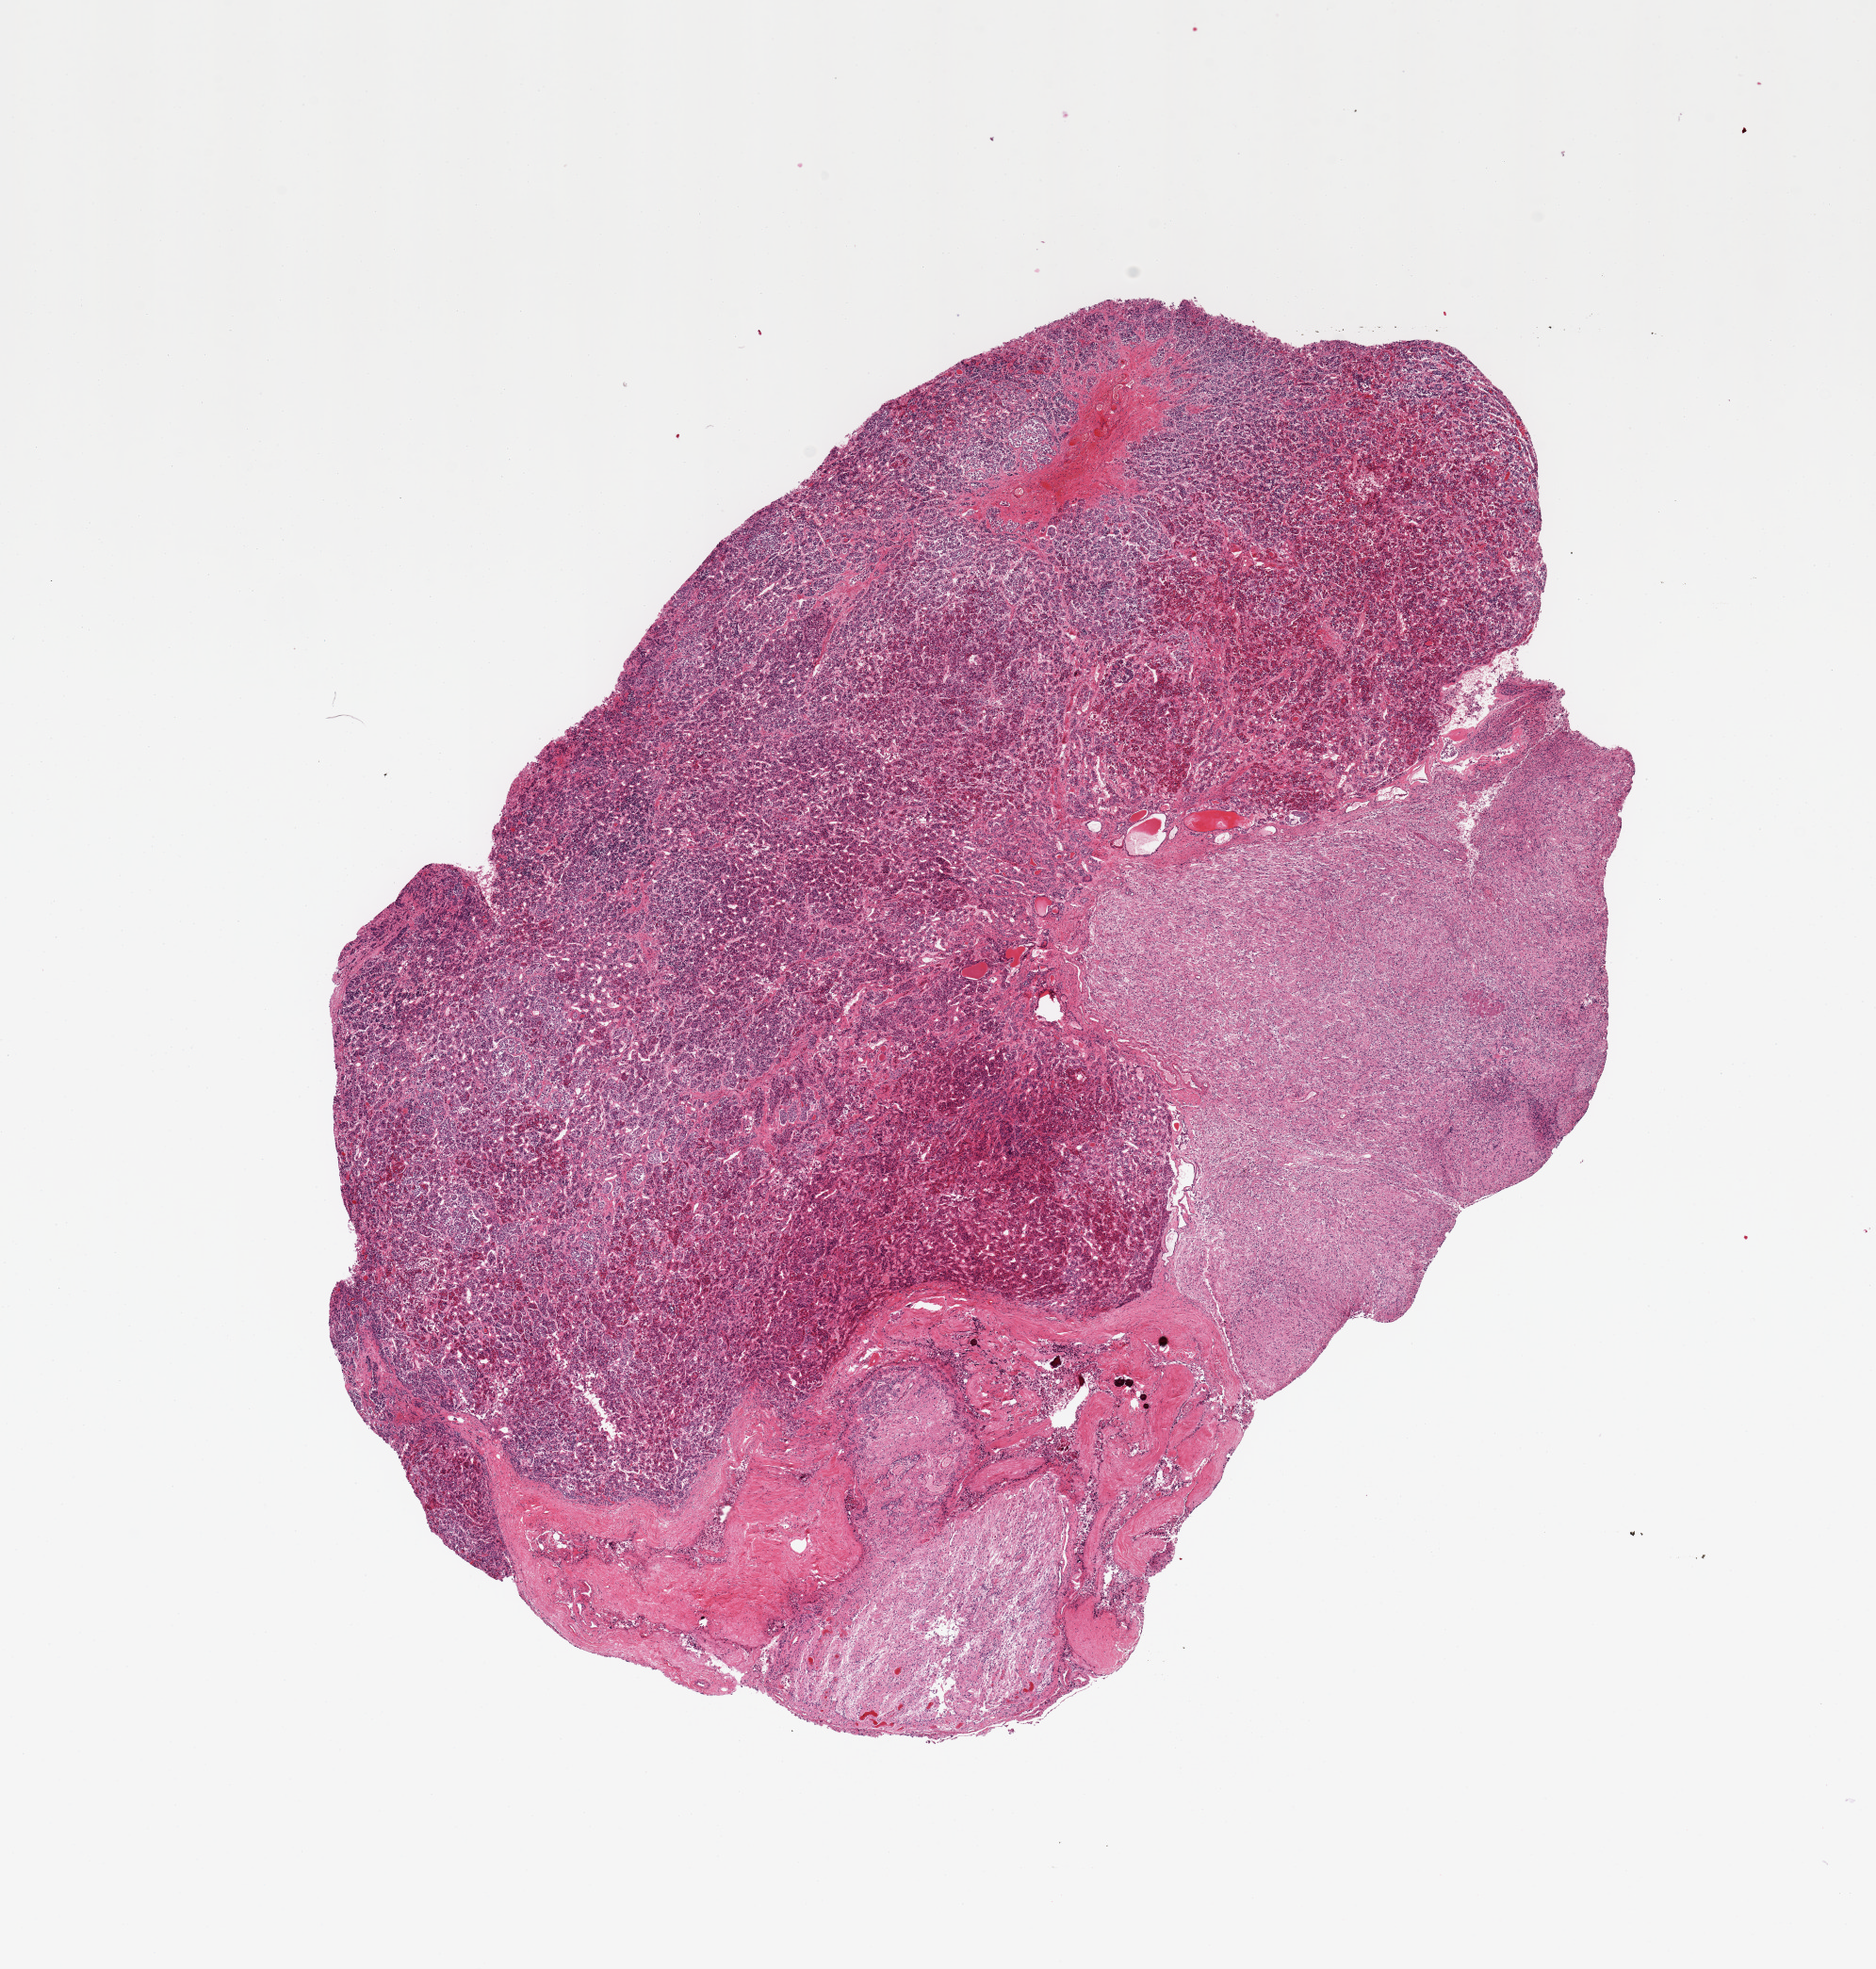
Digitized haematoxylin and eosin-stained section, brightfield, whole scanned area (about 15.8 x 16.5 mm) shown as a low-resolution overview, PAXgene-fixed, paraffin-embedded tissue, target tissue: pituitary, tissue donor sample.
Reviewer comment on this tissue sample: 1 piece, ~70% adenohypophysis, ~20% neurohypophysis, ~10% dura.